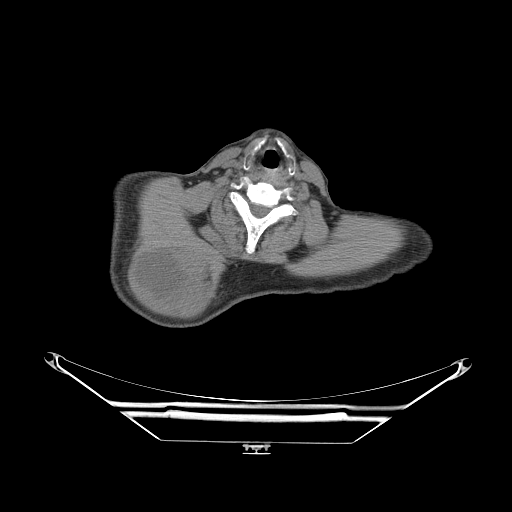
CT of an extremity soft-tissue mass (from a PET/CT study), one axial slice. Reconstruction kernel STANDARD. 140 kVp. Soft-tissue window (W 400 / L 40 HU). 3.75 mm slice thickness. 512 × 512 image matrix. Male patient. From the clinical record (not read from this slice): histological type: pleiomorphic spindle cell undifferentiated; grade: high; site of the primary tumour: right parascapusular.
Annotated regions visible in this slice (expert contour drawn on MRI and transferred to this co-registered scan by the dataset authors):
- gross tumour volume including surrounding oedema: box from (x=130, y=244) to (x=227, y=314) px
- gross tumour volume (mass): (x=133, y=251)–(x=199, y=311)